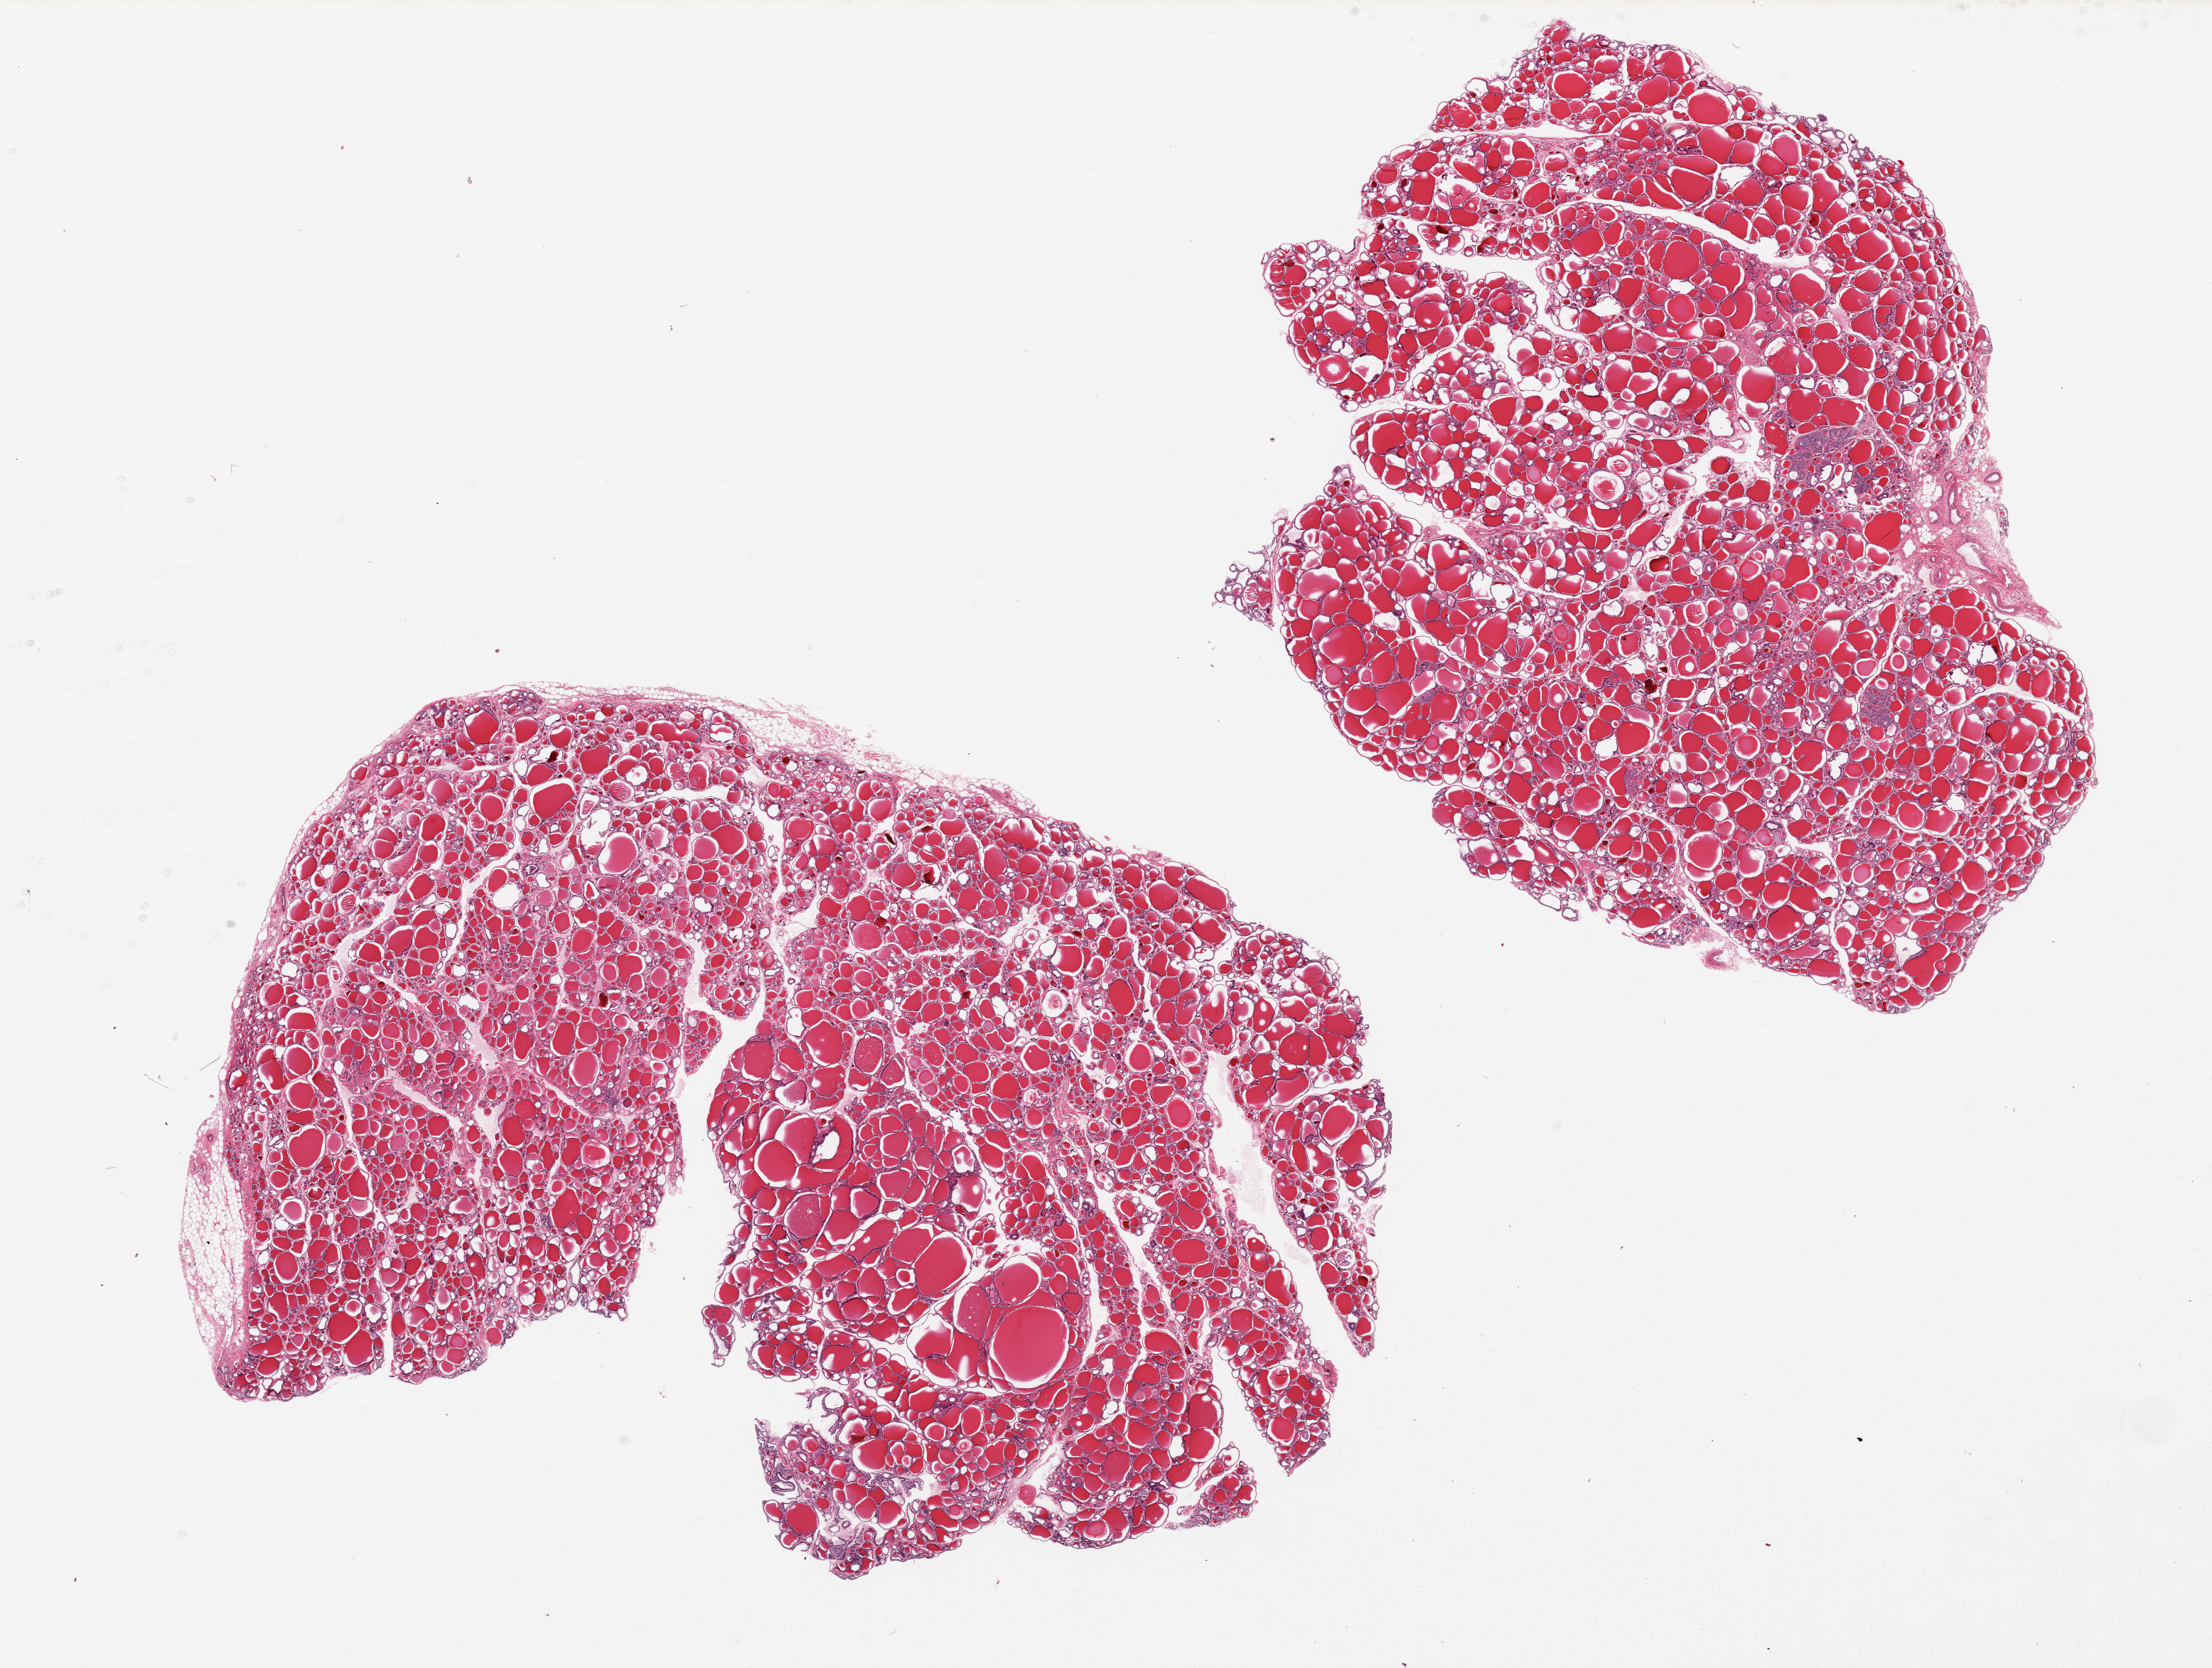
Whole-slide image, H&E stain, low-resolution overview of the scanned area, about 24.6 x 18.6 mm (acquisition: 20x scan), PAXgene-fixed paraffin-embedded (PFPE) section, section of thyroid (target tissue), donor tissue sample. Donor: male.
Reviewer comment on this tissue sample: 2 pieces, microscopic foci of papillary carcinoma.